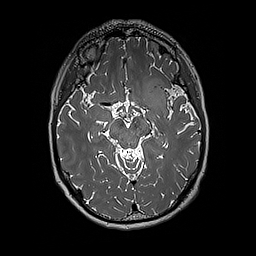
Brain MRI from a brain-tumour surgery series, one axial slice. Slice 112 of 192 in the series (ordered by position). 1 mm slice thickness. 256 × 256 image matrix, field of view 250 × 250 mm. From the clinical record (not read from this slice): histopathology: Glioblastoma; WHO grade: 4; IDH mutation: no.
Annotated regions visible in this slice (manually delineated by an expert):
- tumour: bounding box [x1, y1, x2, y2] px = [140, 78, 171, 112]